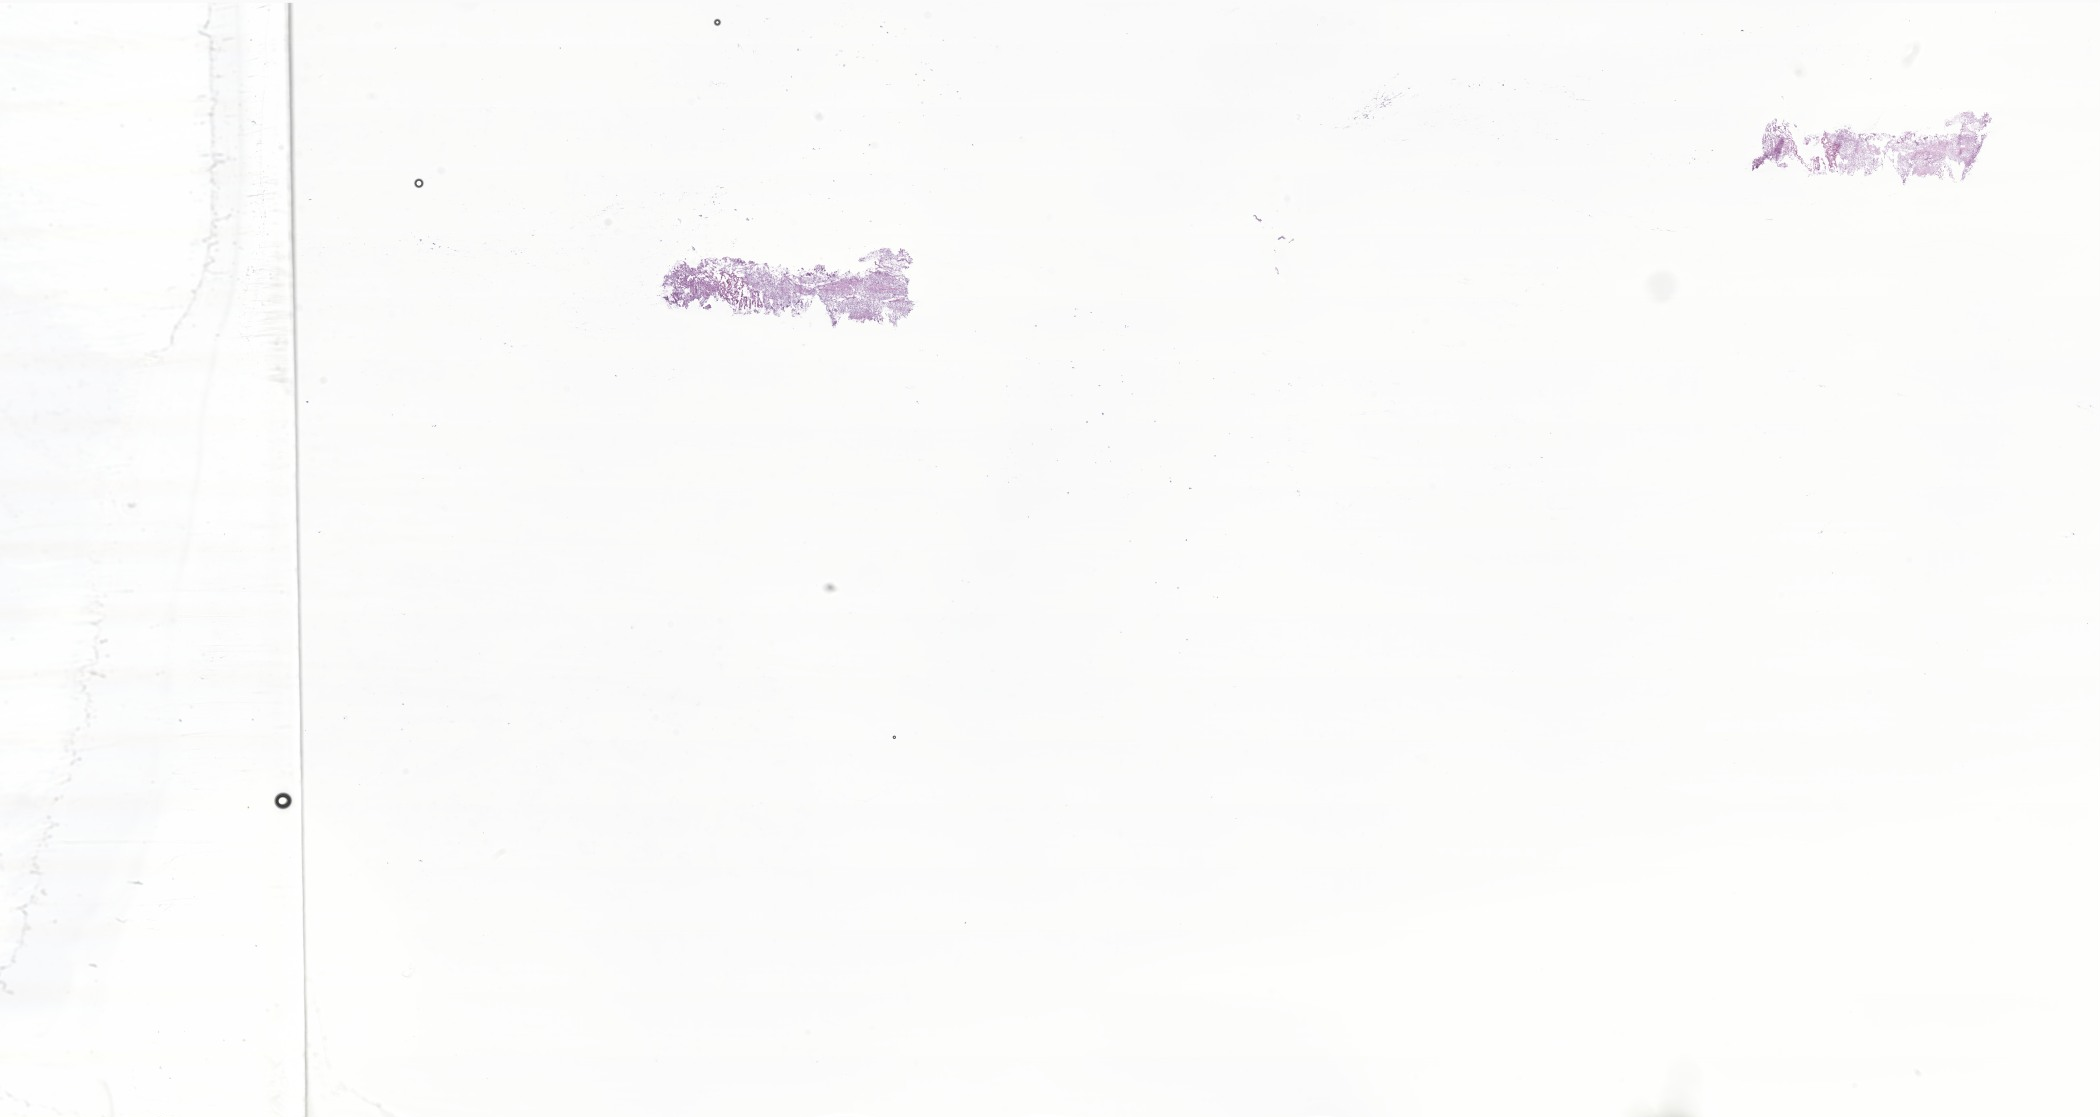
Whole-slide image, hematoxylin and eosin (H&E) stain of tumor tissue from the cerebellum — whole scanned area (about 35.4 x 18.8 mm) shown as a low-resolution overview; frozen section. Male patient, age 133 months (11 years 1 month).
- diagnosis (ICD-O-3 morphology term): Pilocytic astrocytoma